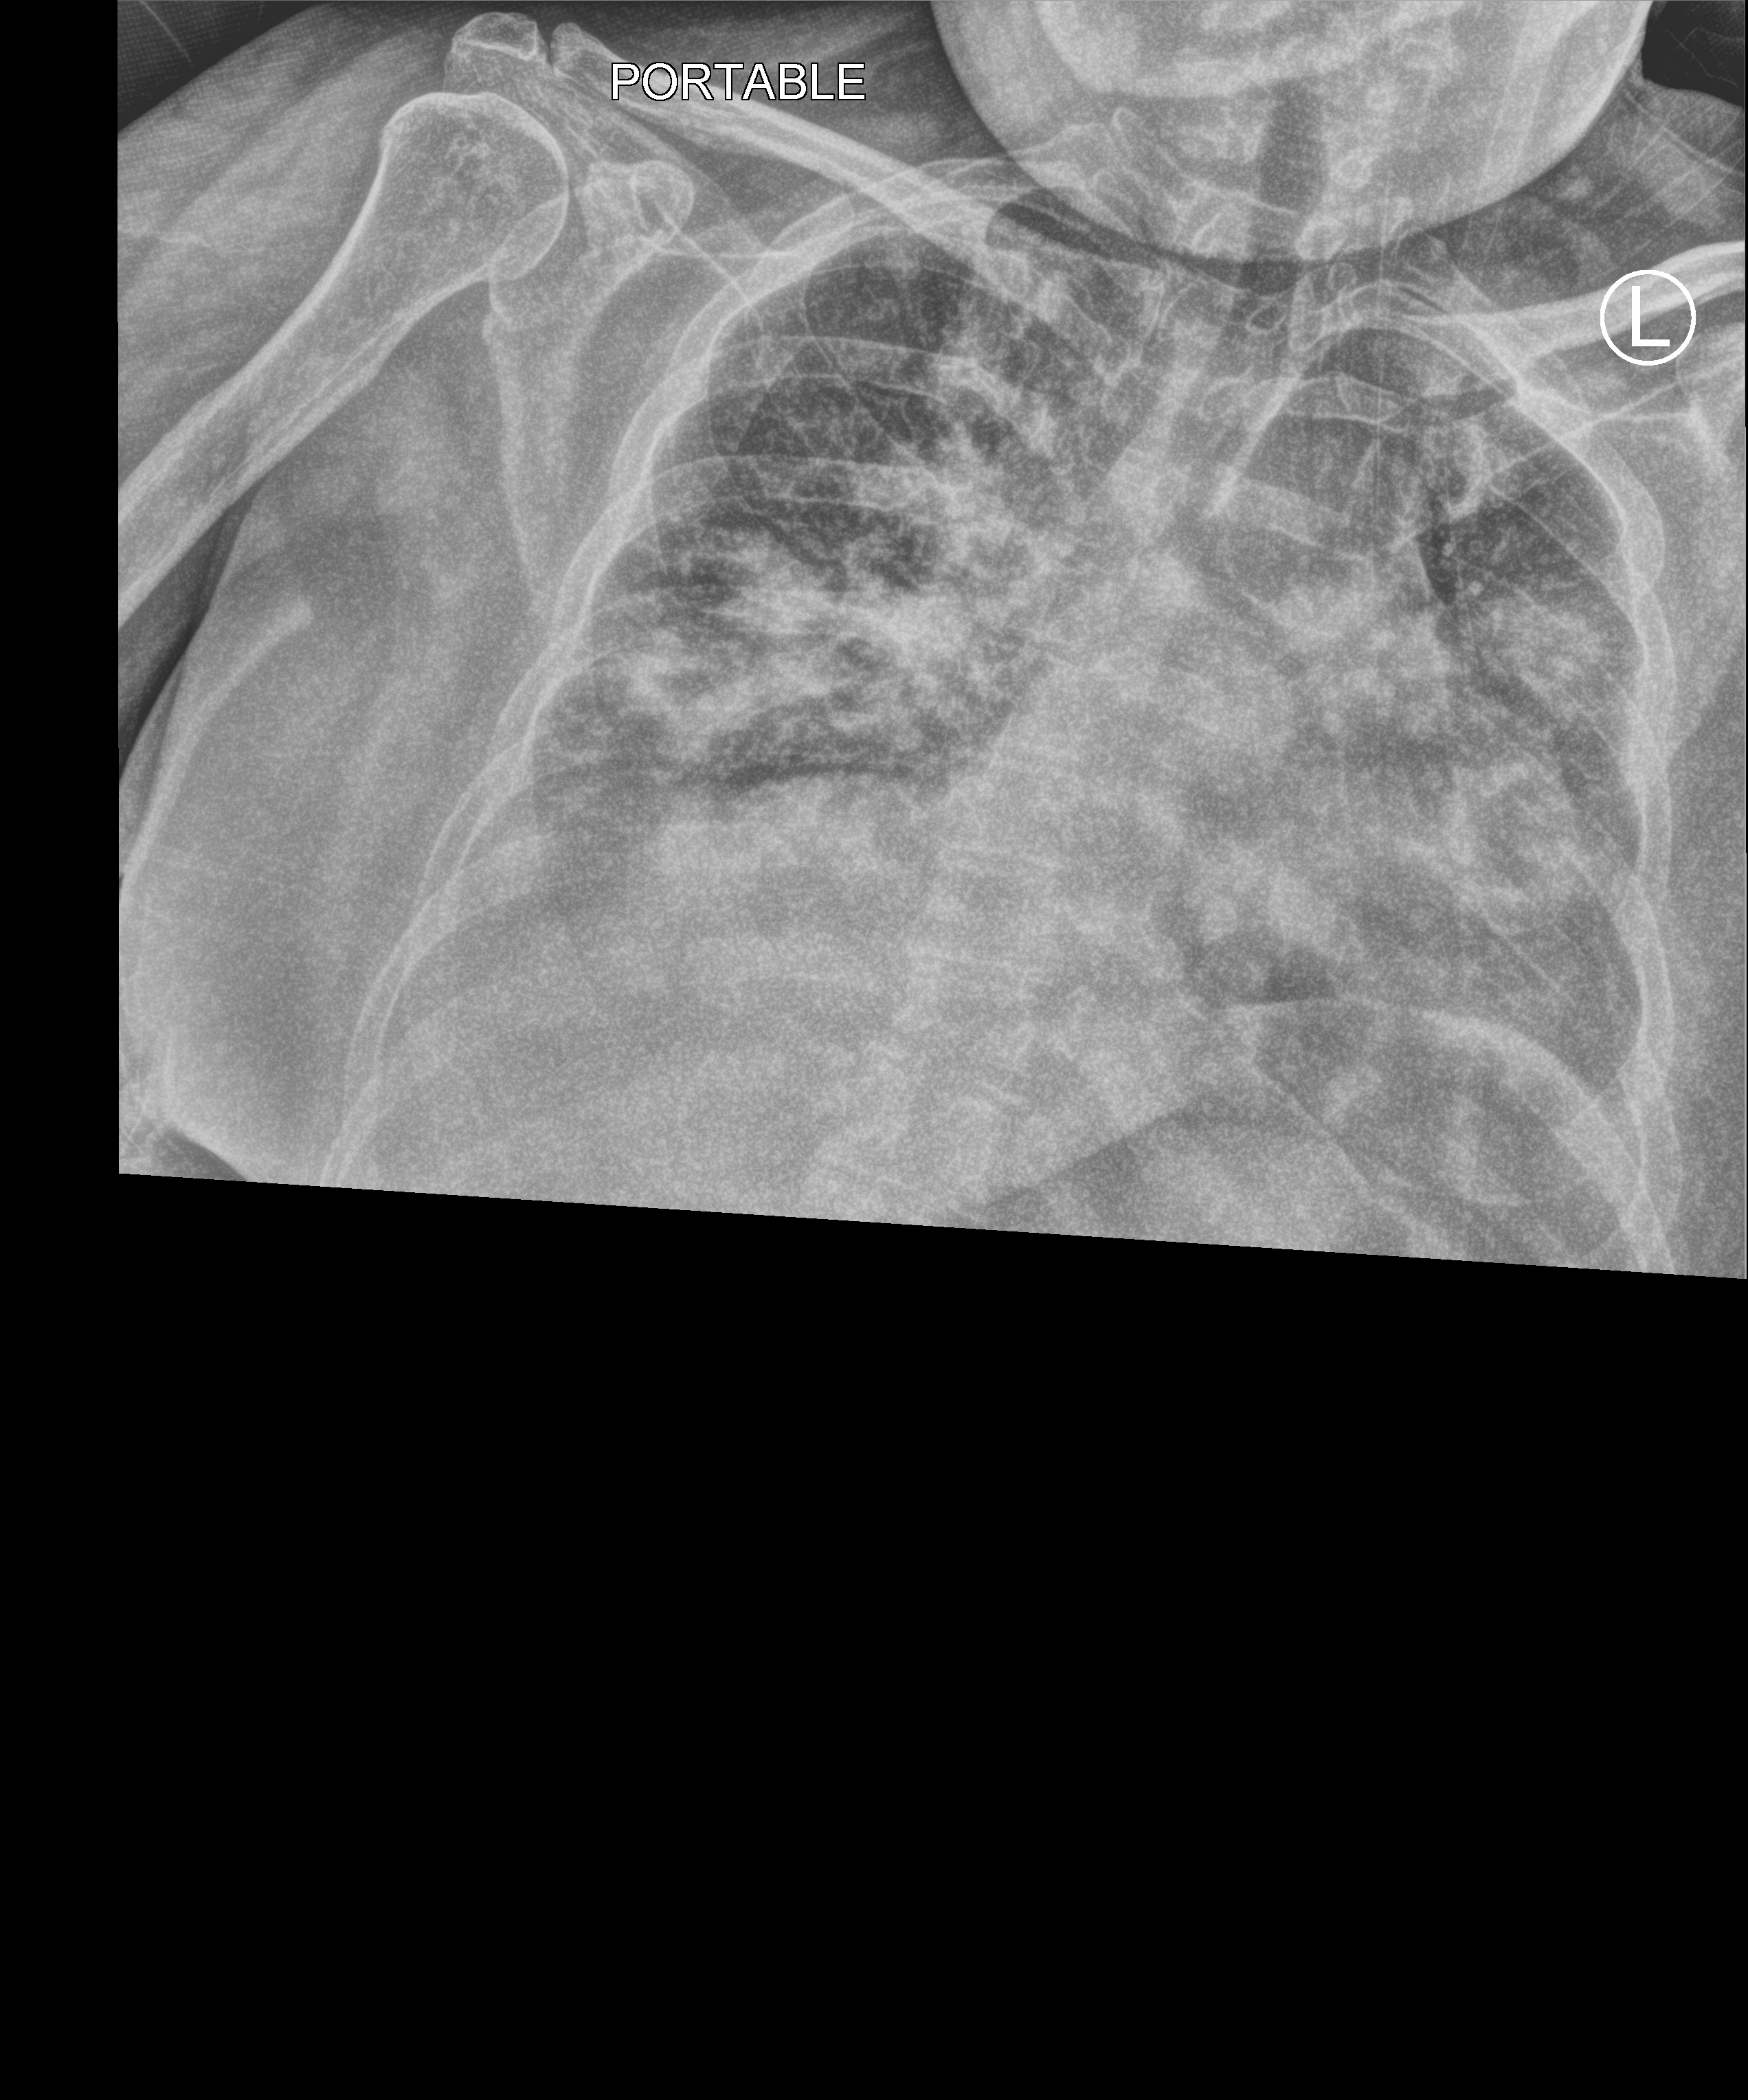
Portable chest radiograph; anteroposterior (AP) projection. Patient hospitalised with COVID-19, aged 18–59 years.
Admission-level facts for this patient (not findings on this image; timing relative to this image not recorded): admitted to intensive care during this hospital stay: yes.